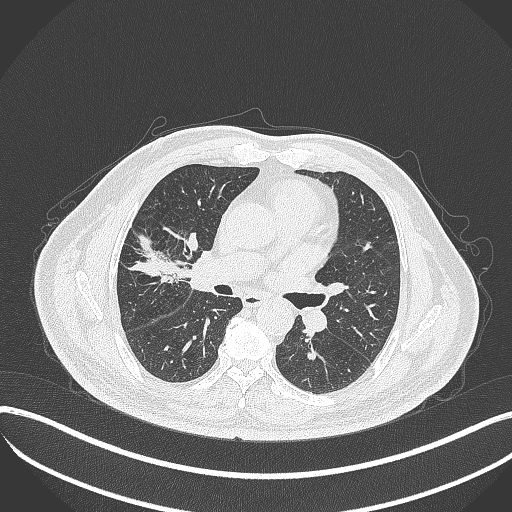
Chest CT, one axial slice. Slice 200 of 401 in the series (ordered by position). Reconstruction kernel B70f. Lung window (W 1500 / L -600 HU). 512 × 512 image matrix, field of view 400 × 400 mm. Patient: male, 72 years. From the clinical record (not read from this slice): clinical TNM (as recorded): T1c N0 M0.
Outlined on this slice (rectangle marked by the reading radiologist):
- lung tumour (recorded histology: squamous cell carcinoma): bounding box (x1, y1, x2, y2) in pixels: (171, 225, 207, 294)